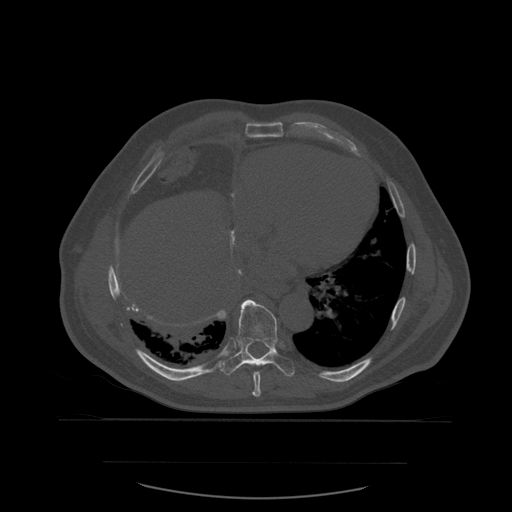
CT including the spine, one axial slice. Slice 345 of 590 in the series (ordered by position). Bone window (W 1800 / L 400 HU). 1.25 mm slice thickness. 512 × 512 image matrix, field of view 479 × 479 mm. Patient age 71 years. Case-level facts recorded for this patient, not image findings: primary cancer: lung; vertebrae with lytic lesions (as recorded): T1, T2, L5, S1.
Structures marked on this image (semi-automatic segmentation, software-assisted and operator-edited):
- T8 vertebra: box from (x=253, y=372) to (x=262, y=397) px
- T9 vertebra: (x=220, y=300)–(x=295, y=377)